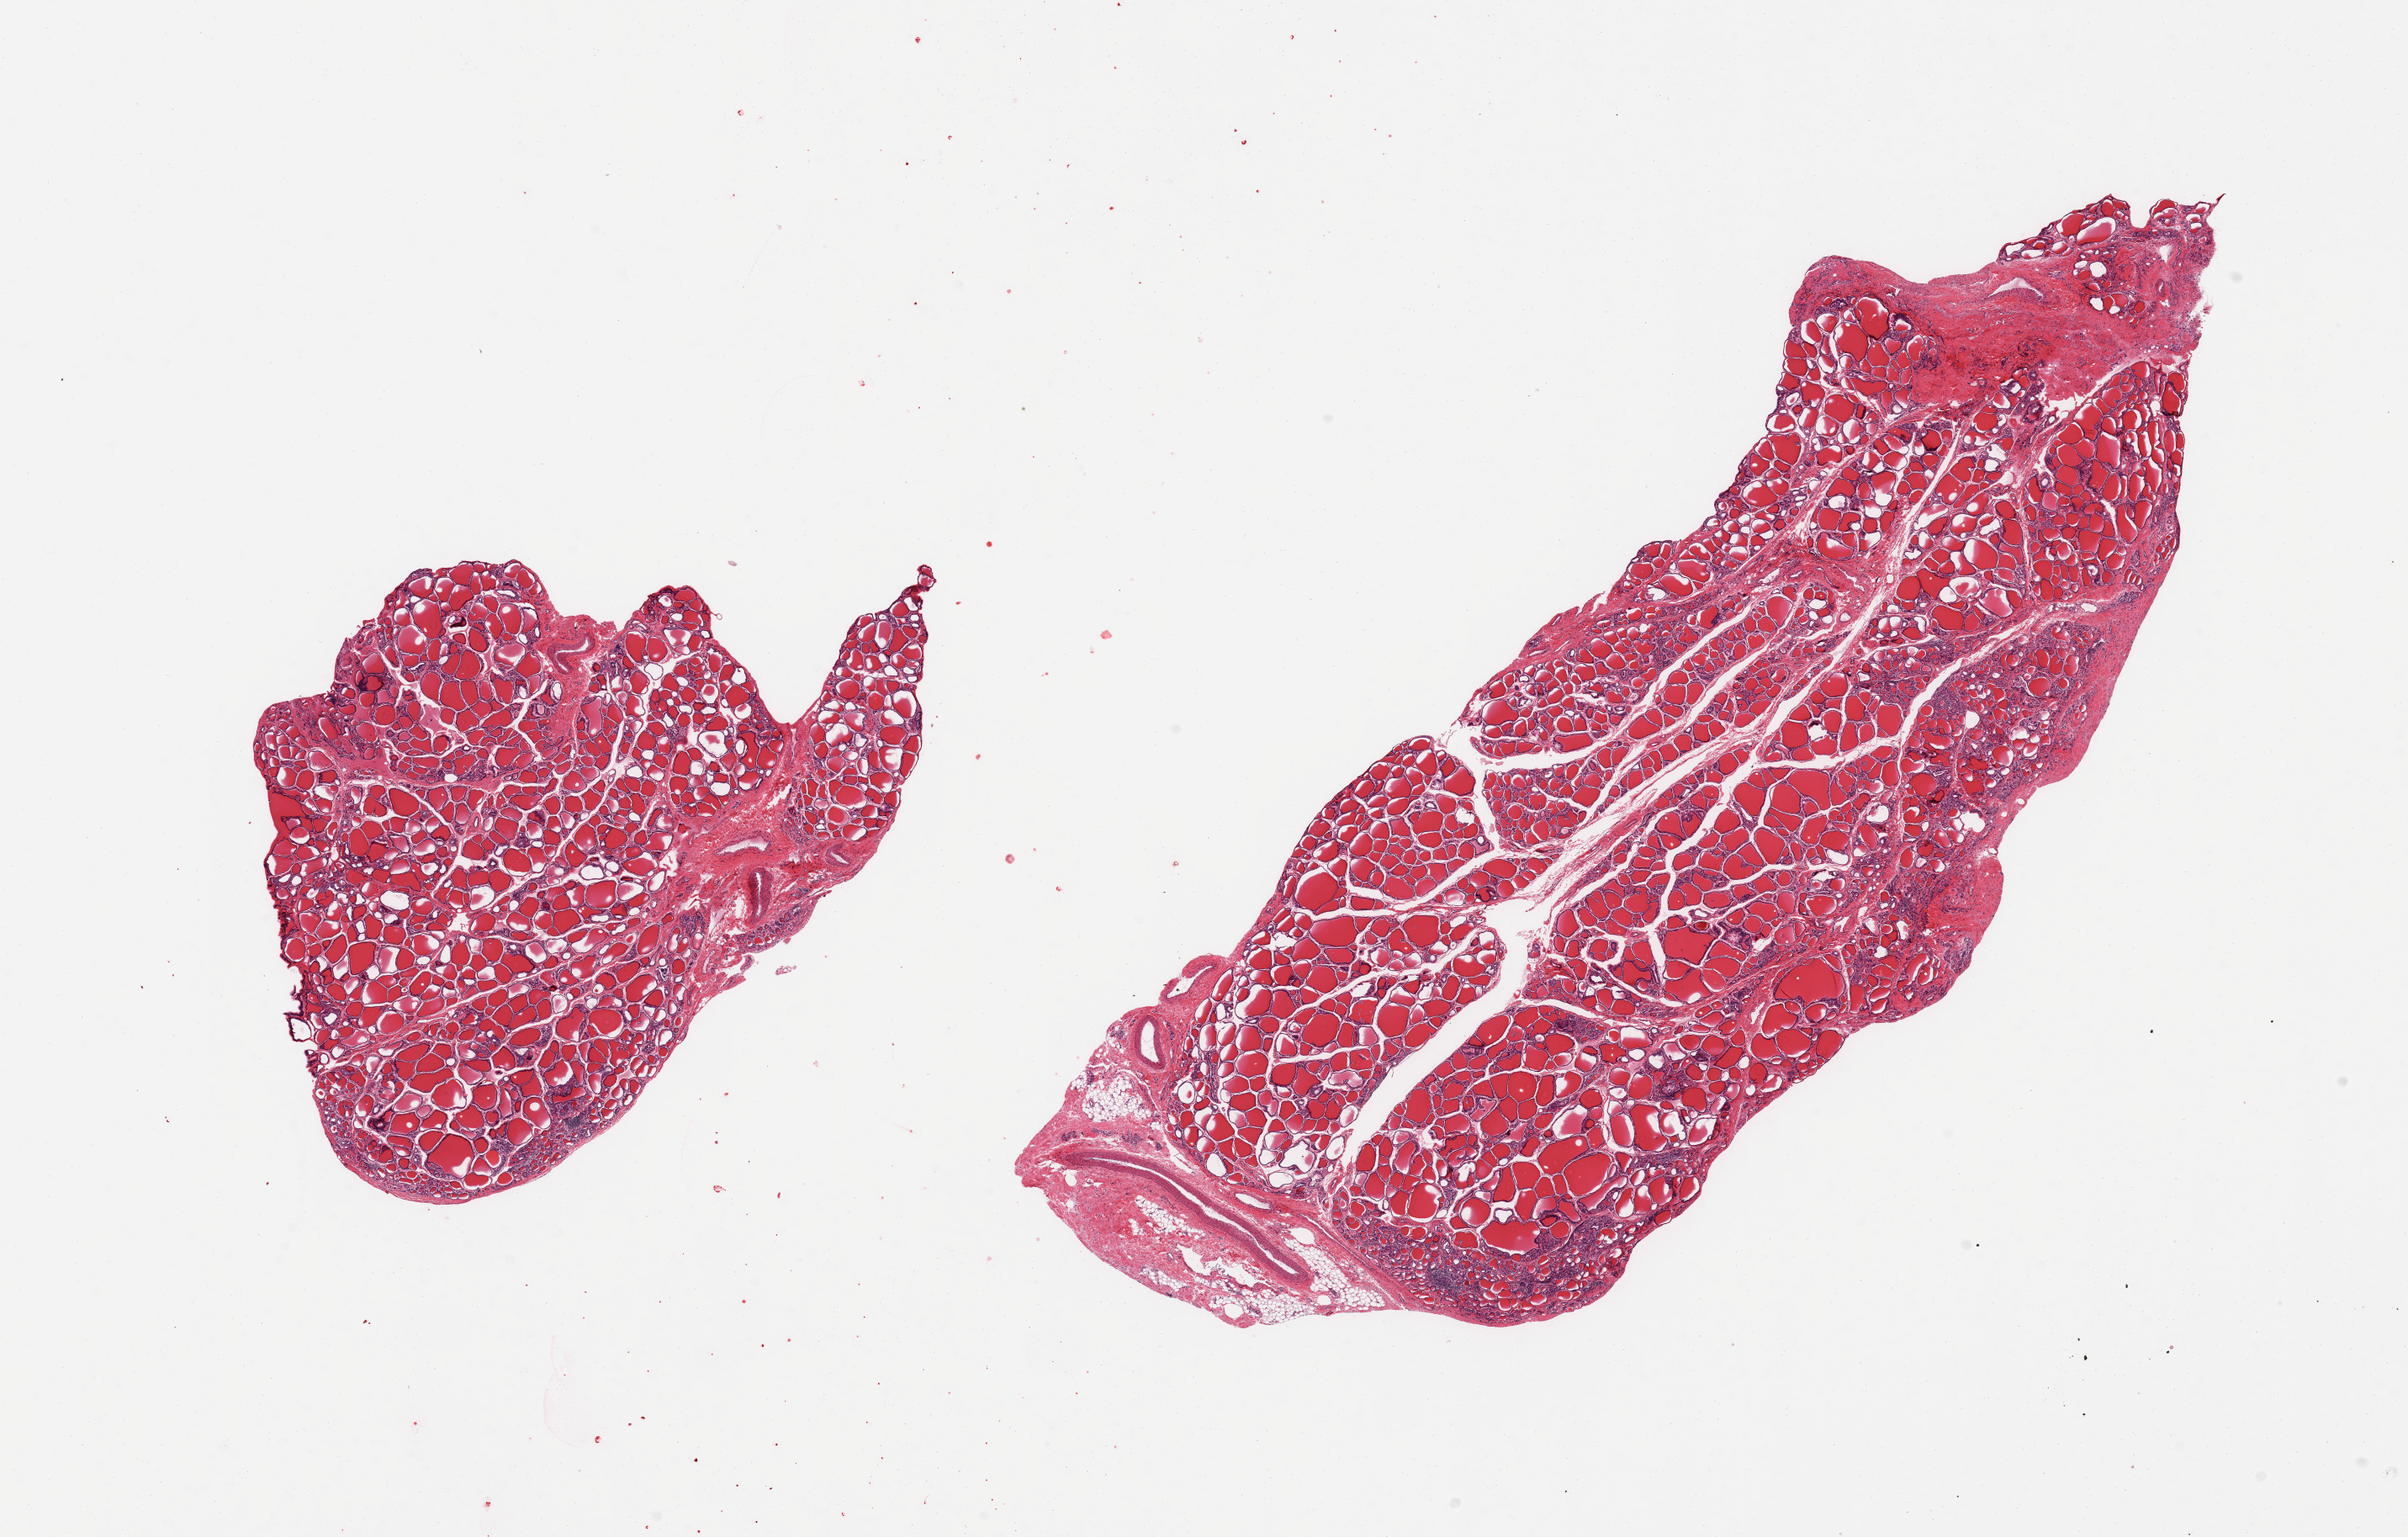
Digitized H&E-stained section, shown as a low-resolution overview of the whole scanned area (about 22.6 x 14.4 mm), PAXgene-fixed, paraffin-embedded tissue, sampled site (target tissue): thyroid, donor tissue sample. Donor sex: male.
- review note (as recorded): 2 pieces, no abnormalities